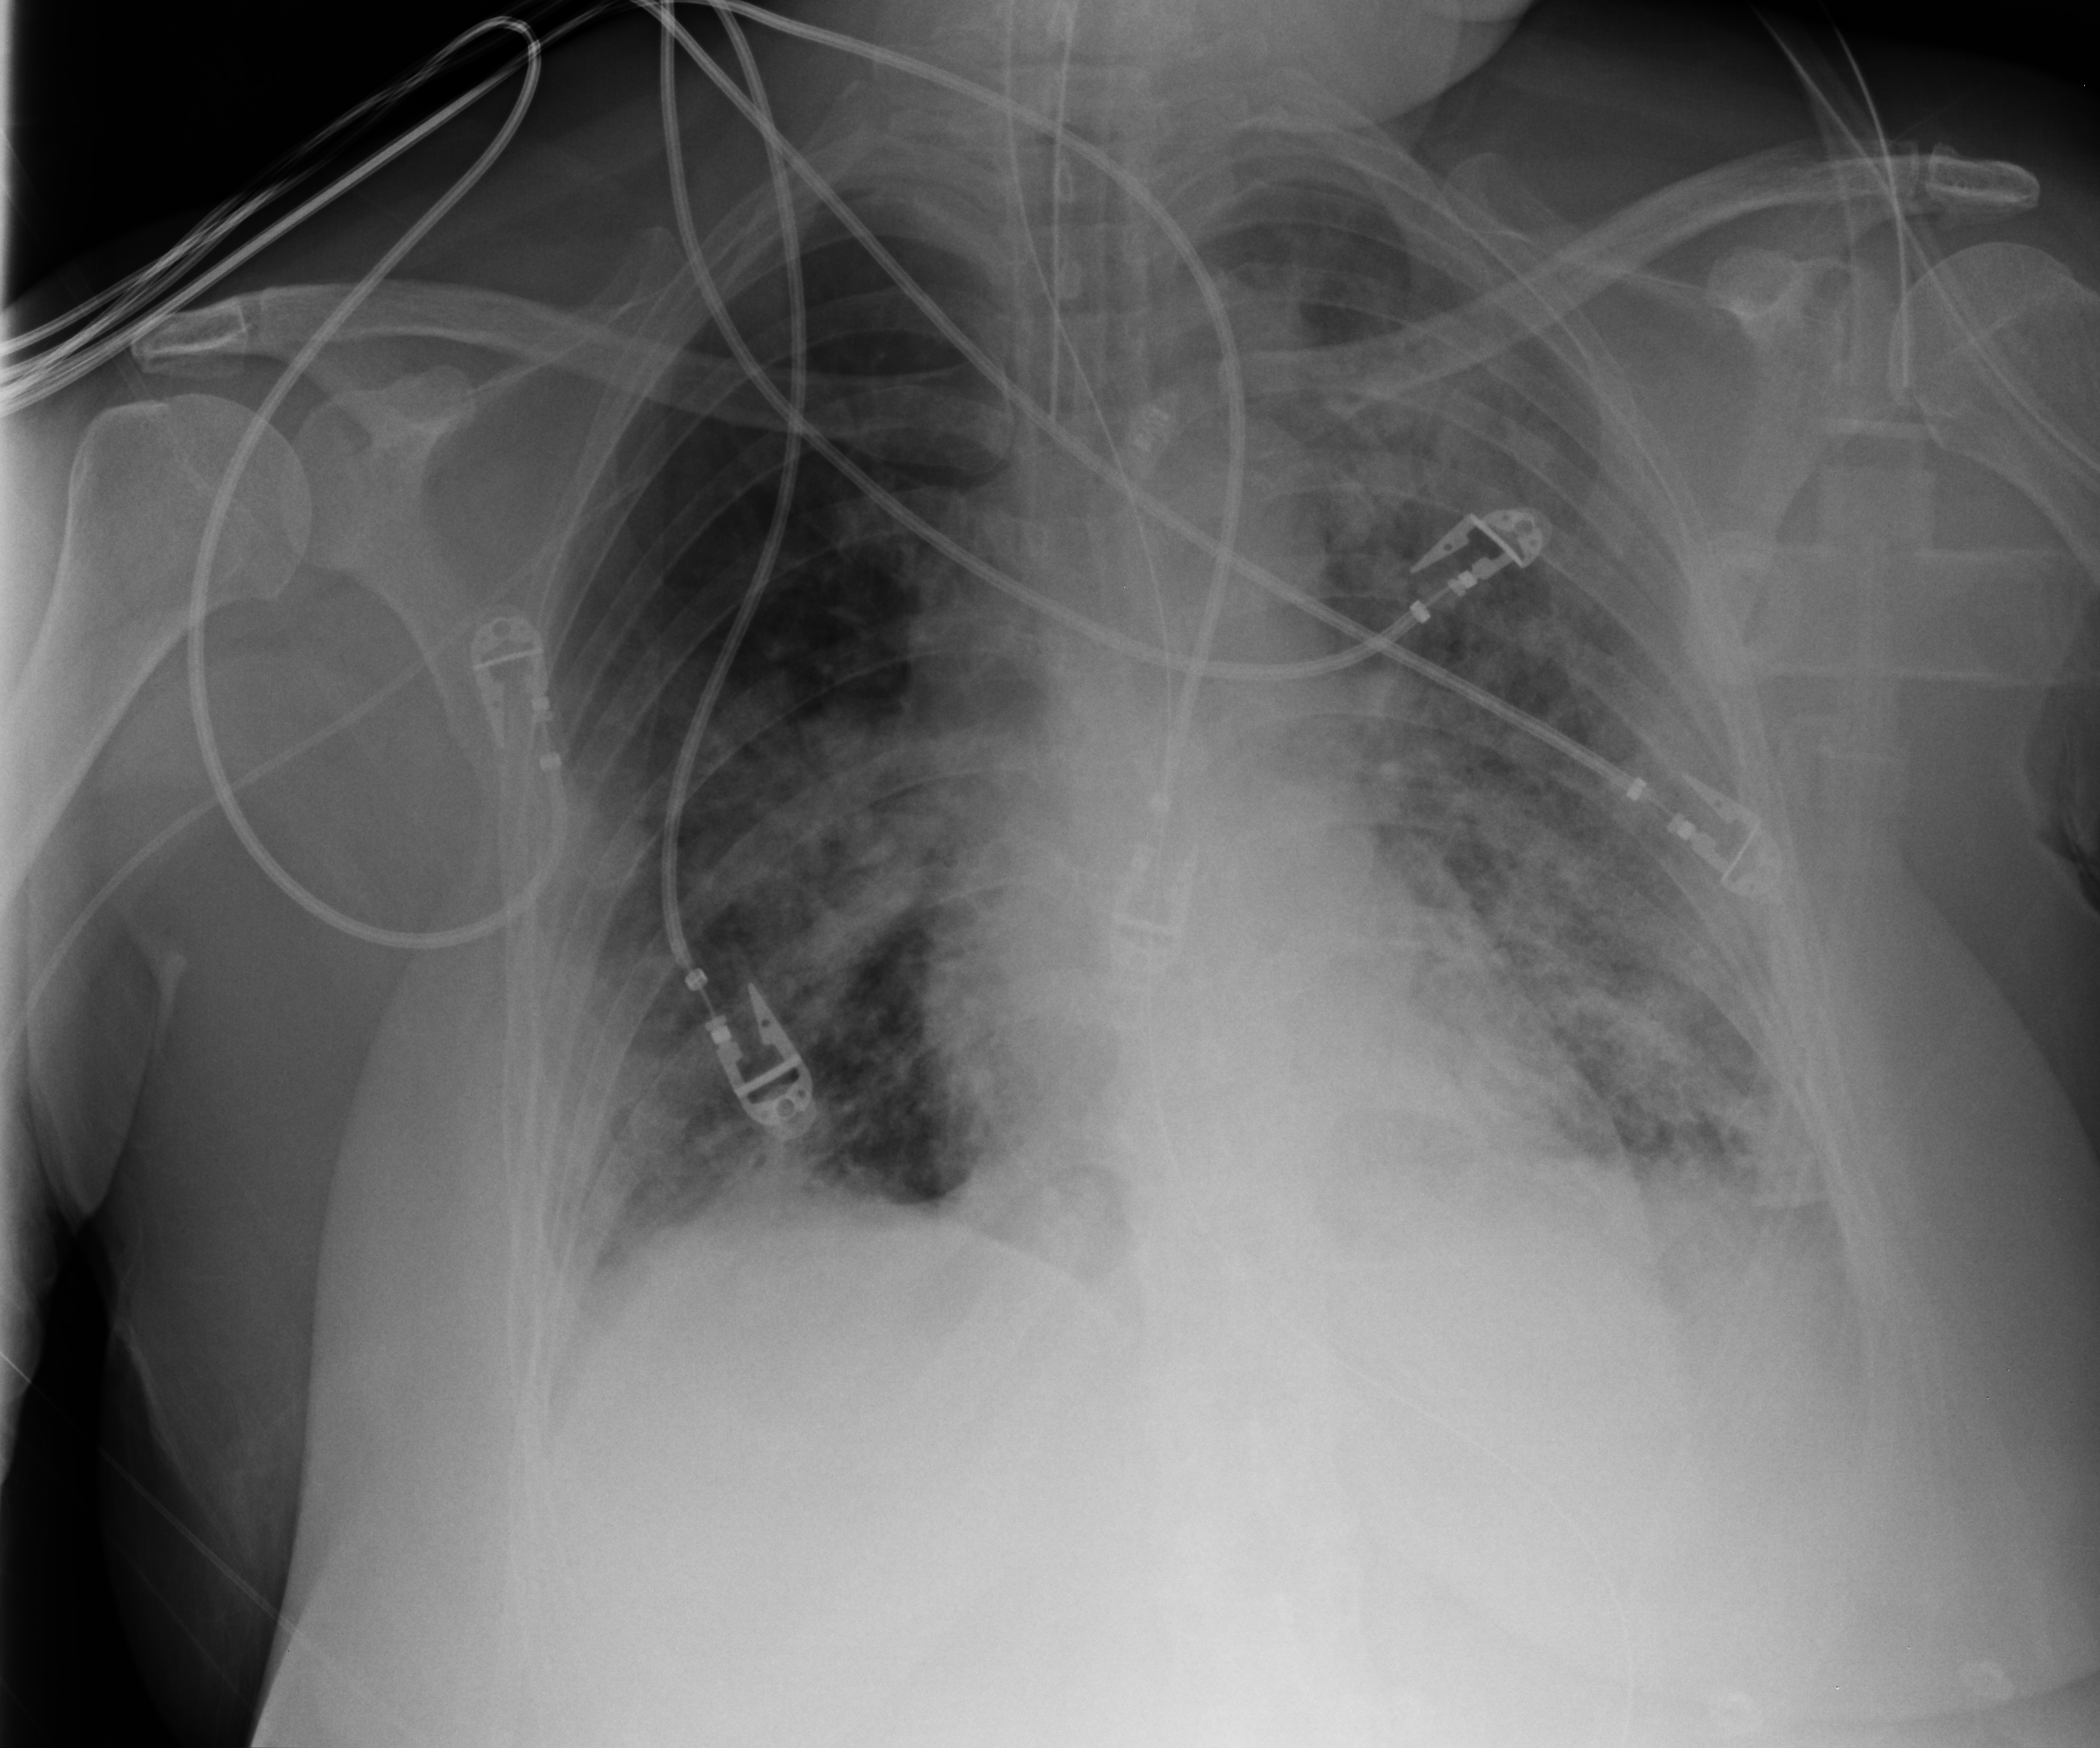
Chest X-ray (portable). Female patient hospitalised with COVID-19, age 18–59 years.
Admission-level facts for this patient (not findings on this image; timing relative to this image not recorded): admitted to intensive care during this hospital stay: yes; mechanically ventilated during this hospital stay: yes.